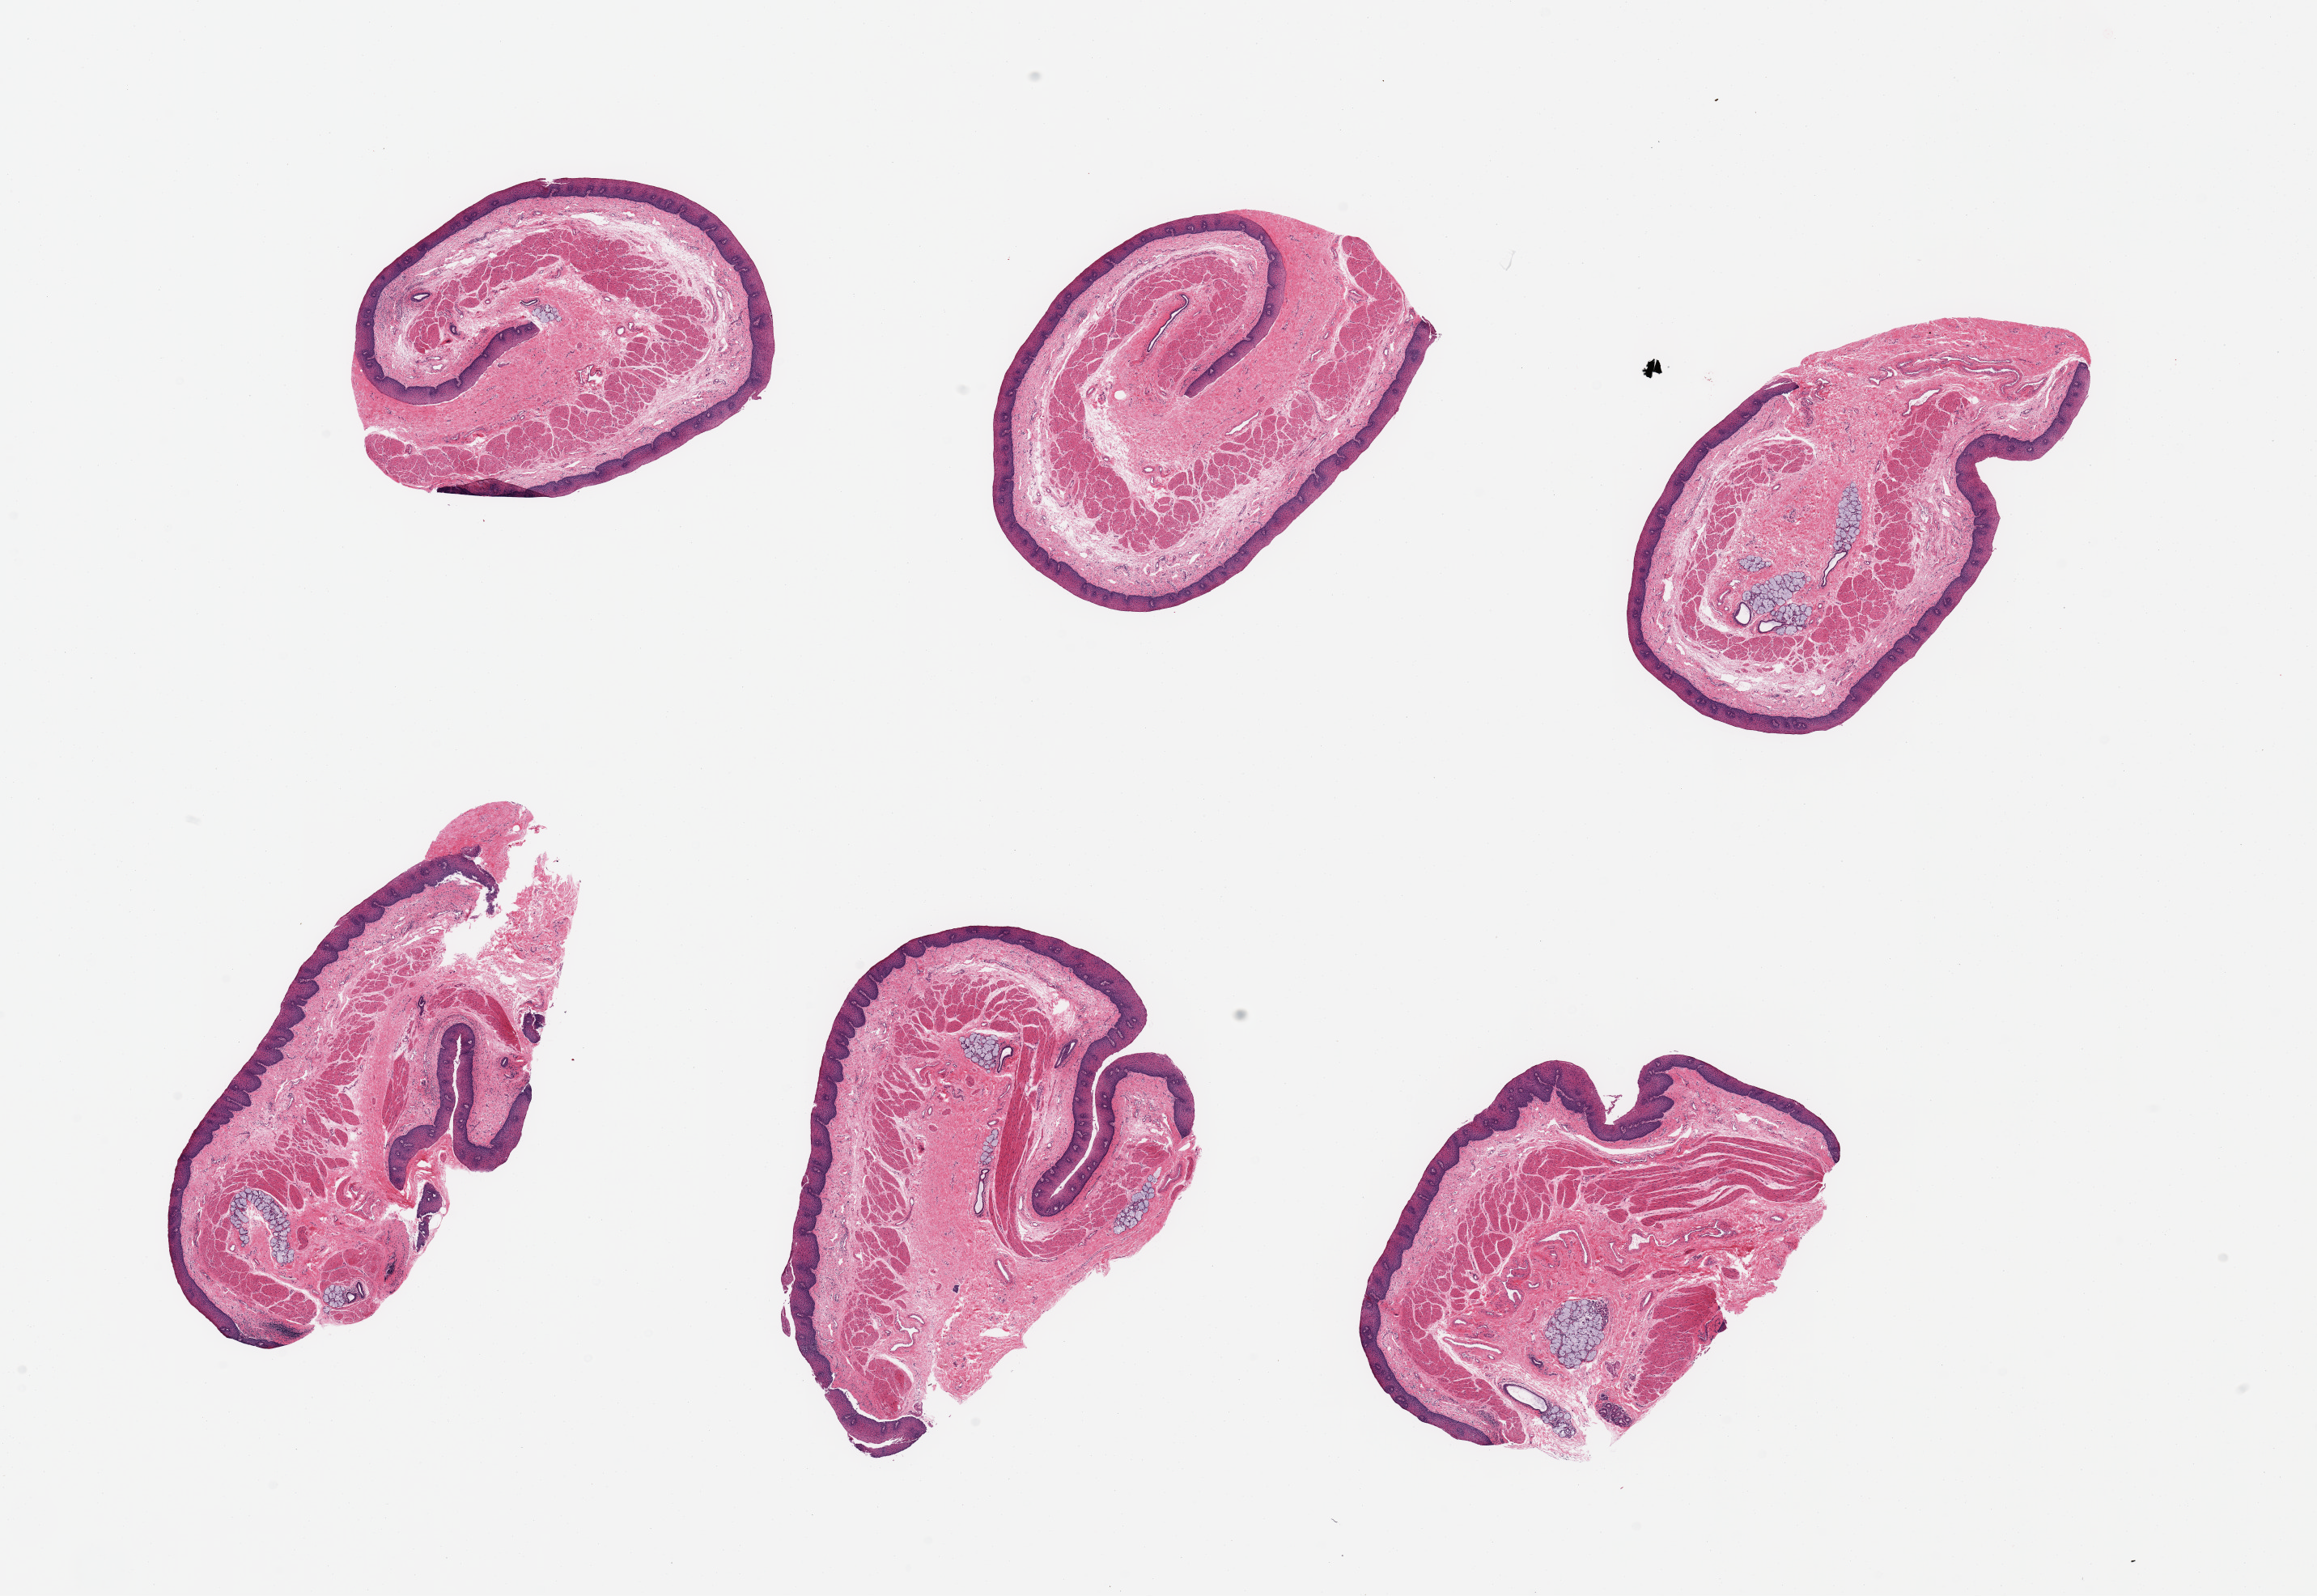
Hematoxylin and eosin (H&E) whole-slide image, brightfield — low-resolution overview of the scanned area, about 22.6 x 15.6 mm (acquisition: 20x scan); PAXgene-fixed paraffin-embedded (PFPE) section; section of esophageal mucous membrane (target tissue); tissue donor sample. Donor: female.
* pathologist's review note for this sample: 6 pieces; ~160 microns thick stratified squamous epithelium; submucosal glands with ducts